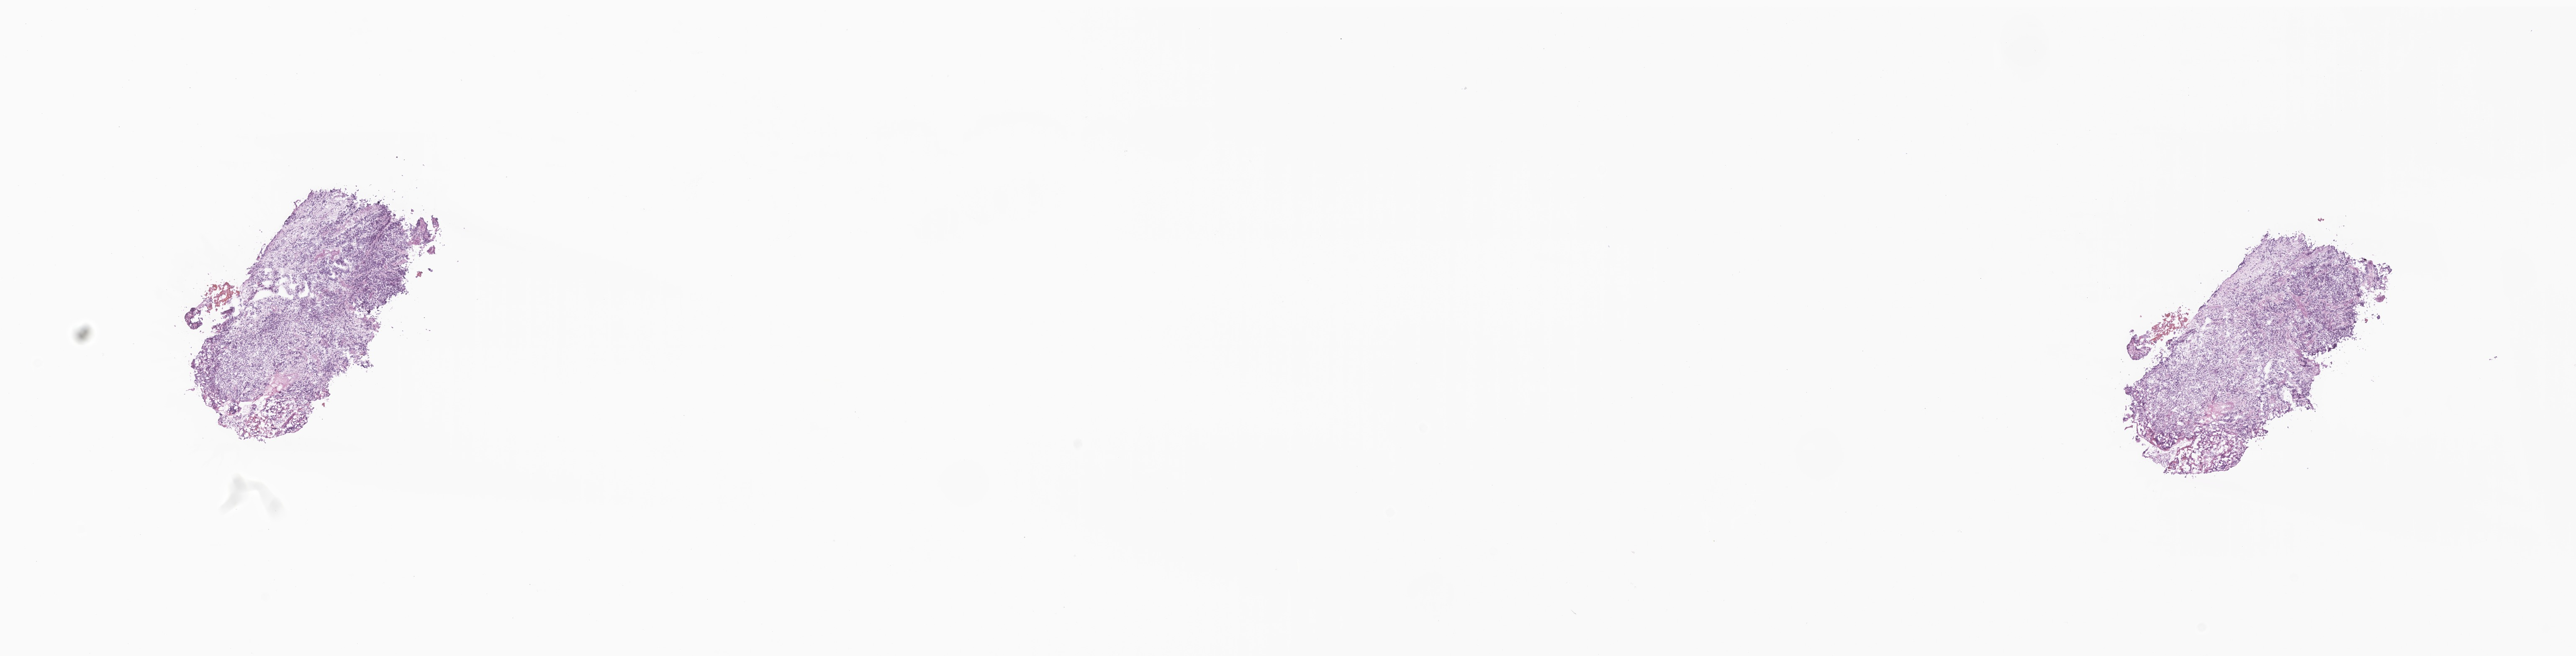
Haematoxylin and eosin whole-slide image of tumor tissue from the brain — low-resolution overview of the scanned area, about 25.9 x 6.6 mm, frozen section (OCT-embedded). Female patient, age 117 months.
Diagnosis: Medulloblastoma, NOS.